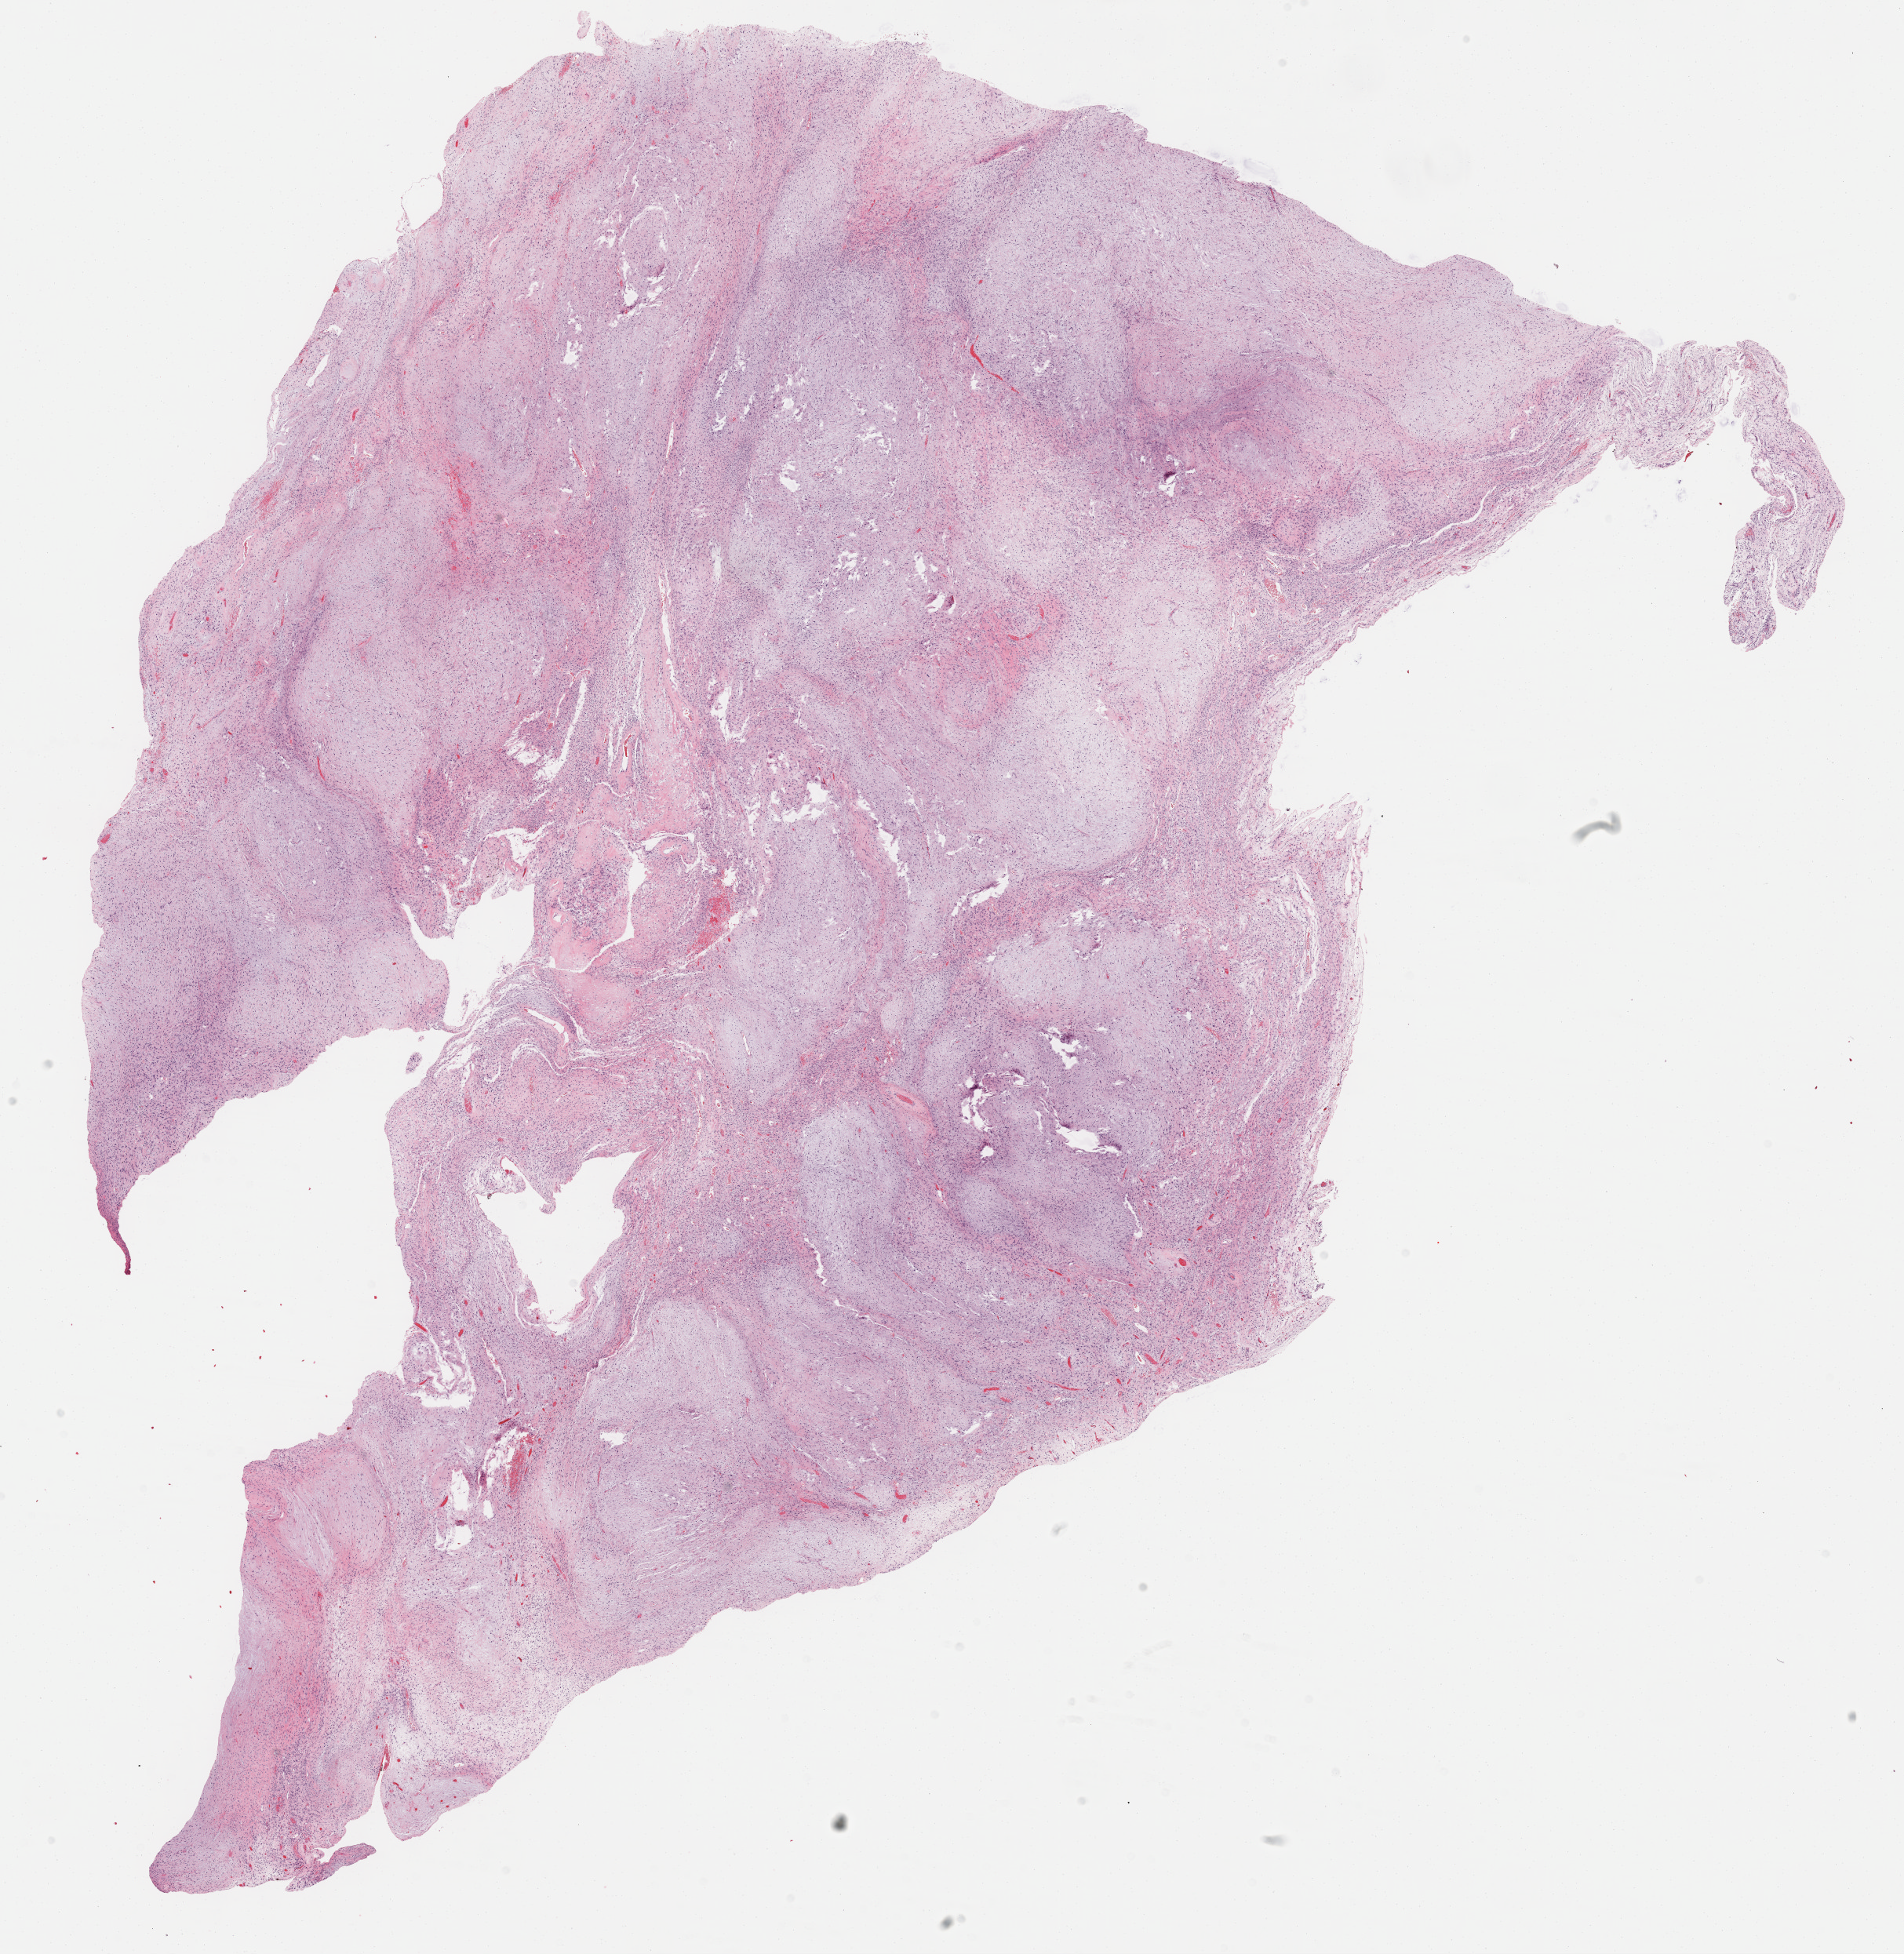
Whole-slide histology image, H&E-stained, low-resolution overview of the scanned area, about 19.6 x 20.1 mm (slide scanned at 40x), formalin-fixed paraffin-embedded (FFPE) diagnostic section, retroperitoneum and peritoneum, primary tumour sample. Male patient; age at initial diagnosis 52 years.
Histologic diagnosis: Undifferentiated sarcoma (retroperitoneum).